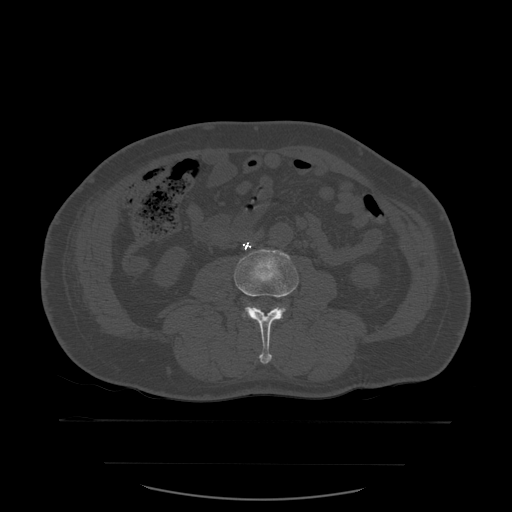
CT including the spine, one axial slice. Slice 187 of 590 in the series (ordered by position). Bone window (W 1800 / L 400 HU). 1.25 mm slice thickness. 512 × 512 image matrix. Patient age 71 years. From the clinical record (not read from this slice): primary cancer: lung; vertebrae with lytic lesions (as recorded): T1, T2, L5, S1.
Outlined on this slice (semi-automatic segmentation, software-assisted and operator-edited):
- L3 vertebra: box from (x=234, y=249) to (x=299, y=364) px
- L4 vertebra: (x=246, y=308)–(x=250, y=315)